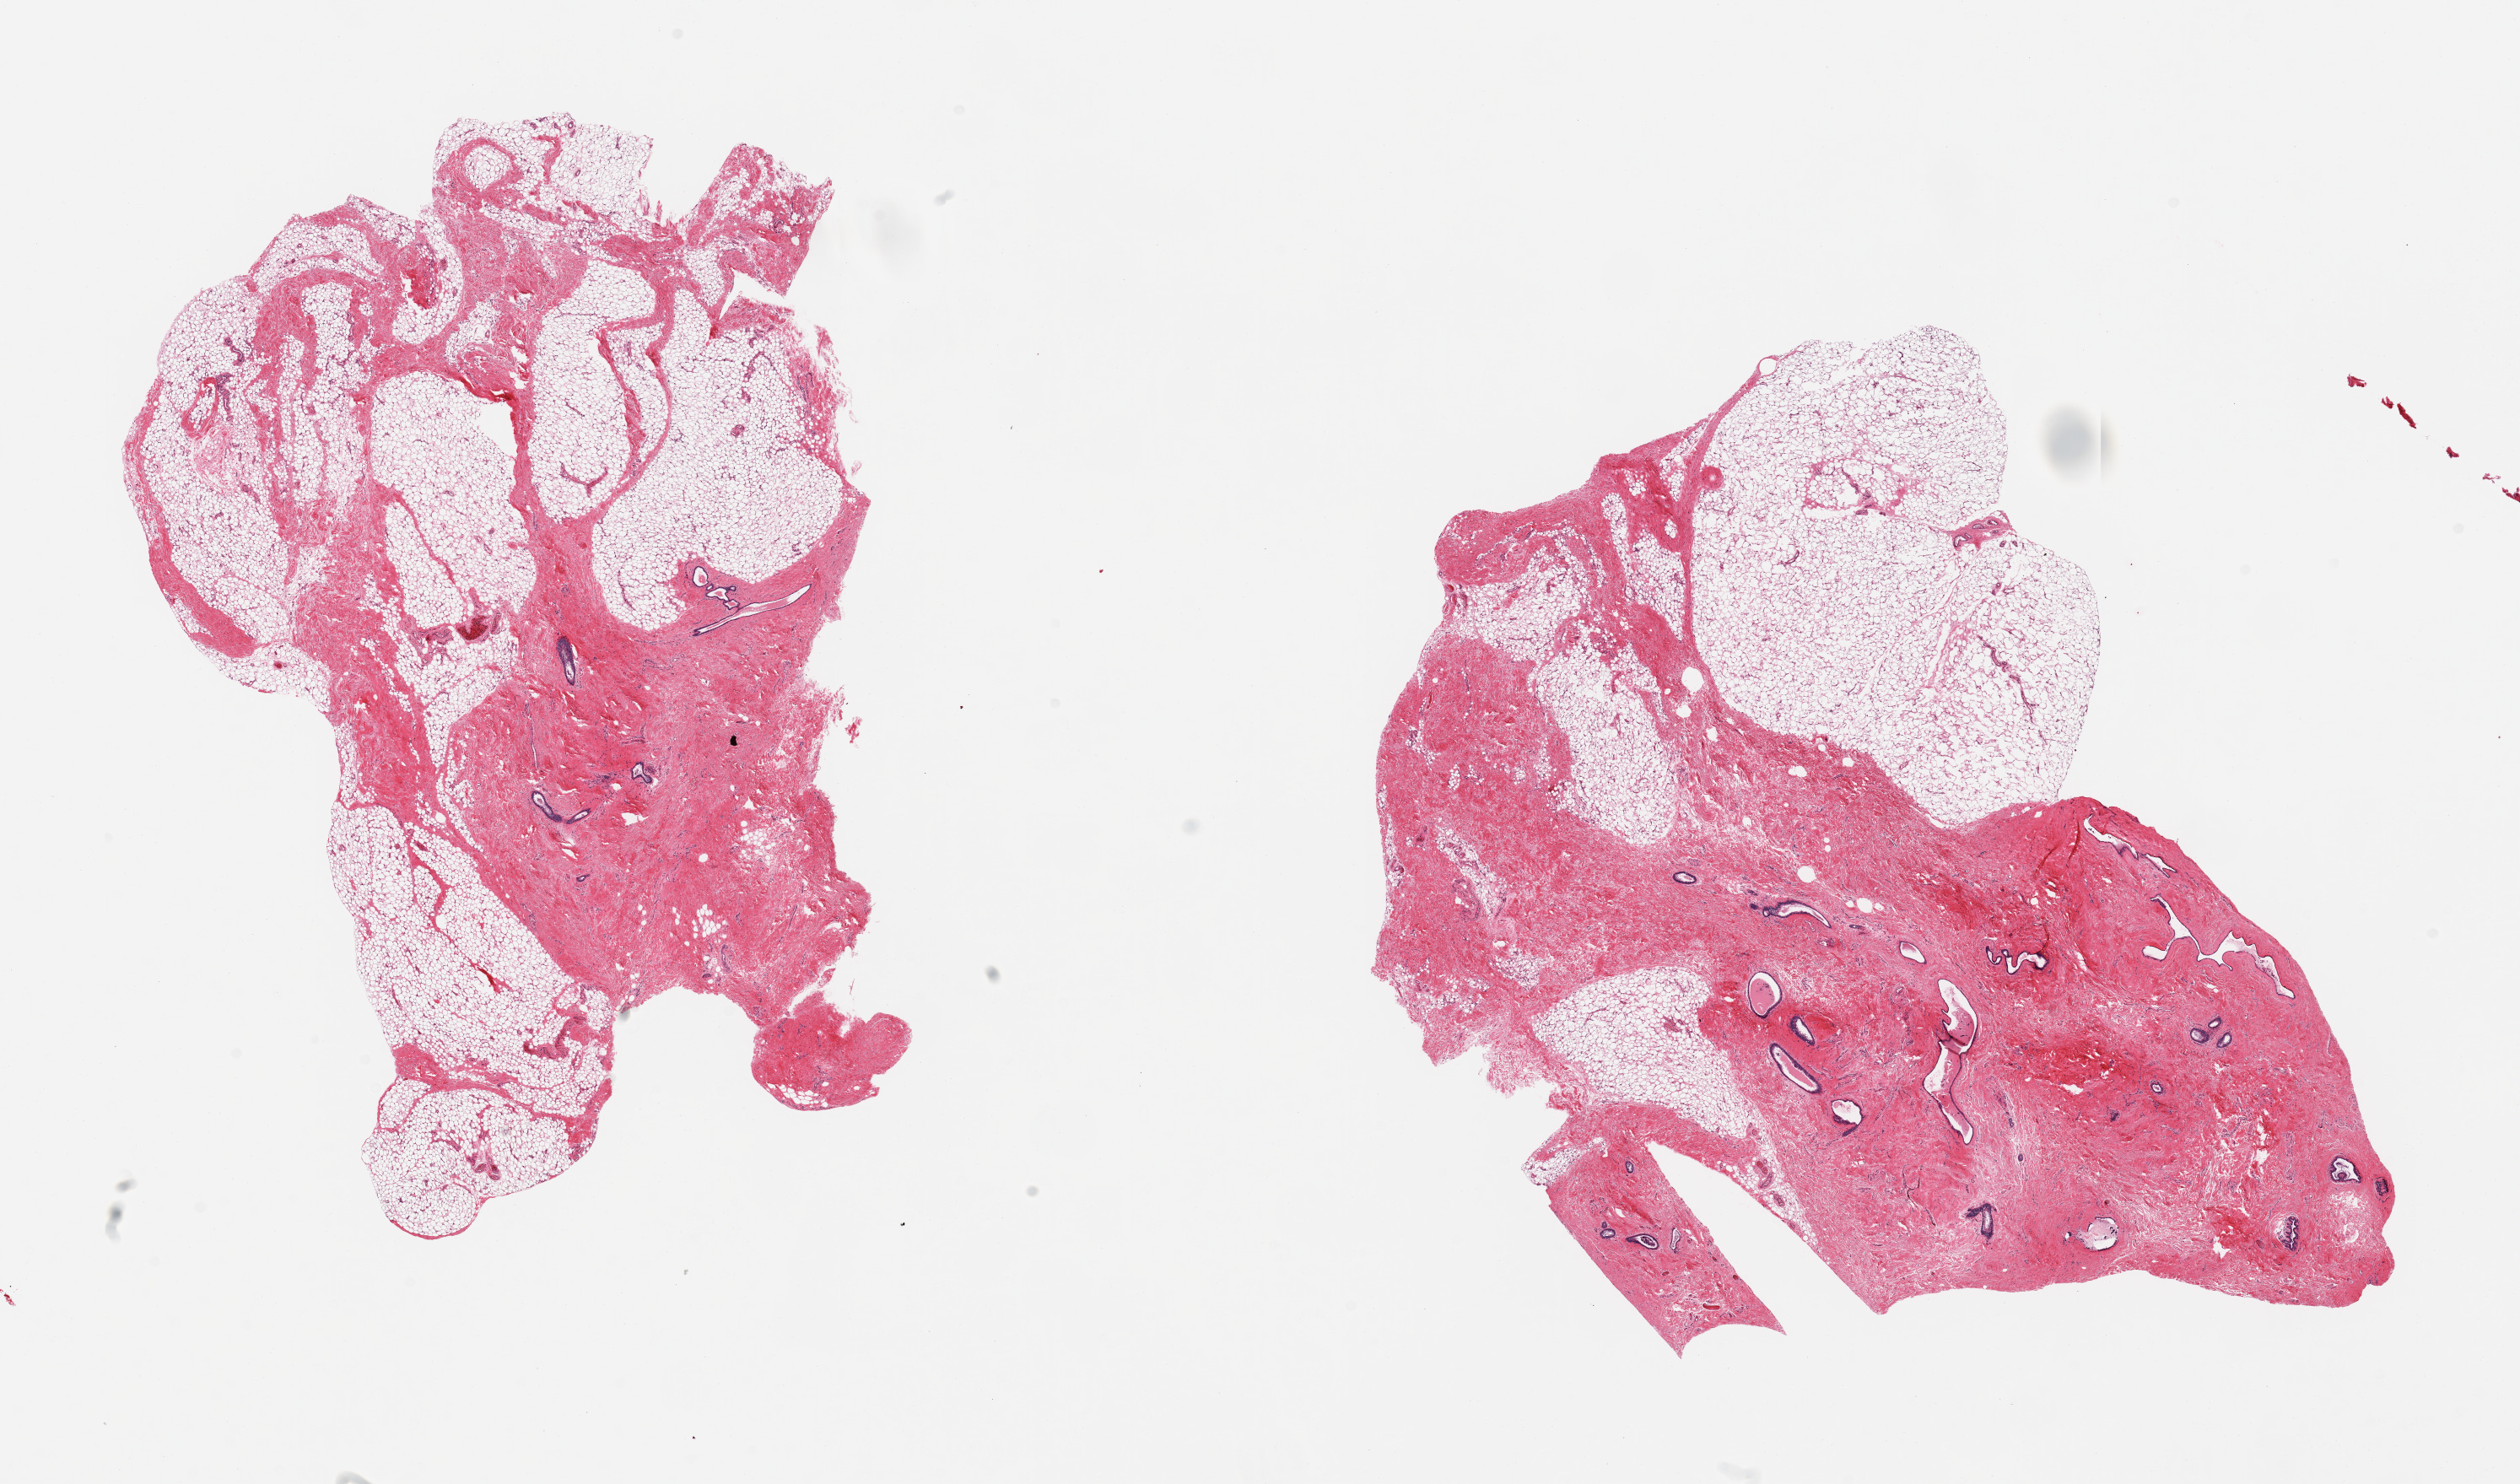
Hematoxylin and eosin (H&E) whole-slide image, brightfield, whole scanned area (about 23.6 x 13.9 mm) shown as a low-resolution overview; PAXgene-fixed paraffin-embedded (PFPE) section; target tissue: breast; donor tissue sample. Donor sex: male.
• pathologist's review note for this sample: 2 pieces; adipose tissue and dense fibrous tissue with embedded ductal structures, some mildly dilated